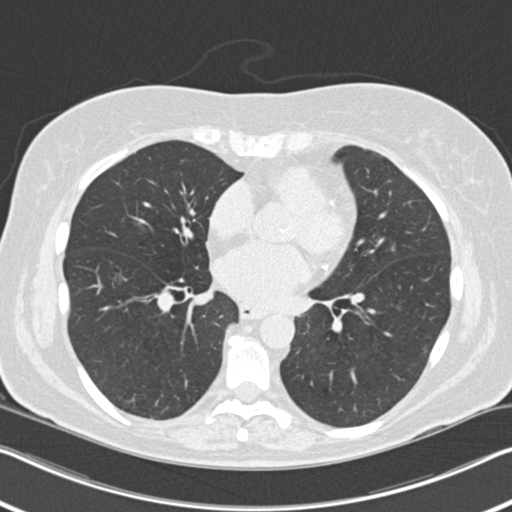
Chest CT (low-dose screening protocol), one axial image, second annual screen, lung window (W 1500 / L -600 HU), 2 mm slice thickness, standard (soft-tissue) reconstruction kernel (B30f), slice 111 of 202 in the series, 512 × 512 image matrix, field of view 336 × 336 mm. Female, age 60 years at enrolment.
Lesion marked by an expert reader, bounding box <375,240,410,270> (left, top, right, bottom; pixels). The screening reader recorded 6 non-calcified nodules or masses ≥4 mm on this exam (right upper lobe, right middle lobe, right lower lobe, right lower lobe, left lower lobe, lingula); which of them this box marks is not recorded. Official screen result: positive, change unspecified: nodule(s) >= 4 mm or enlarging nodule(s), mass(es), or other non-specific abnormalities suspicious for lung cancer. Participant outcome: lung cancer diagnosed 495 days after this screen (after the third annual screen) — non-small cell carcinoma, left upper lobe, poorly differentiated (G3), stage IB (AJCC 6th edition), 7 mm at pathology.